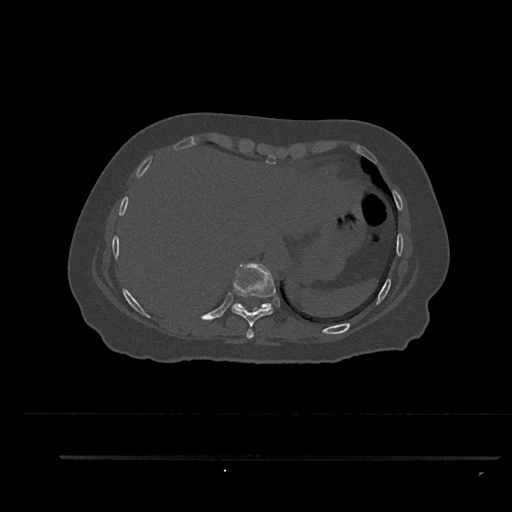
CT including the spine, one axial slice; slice 402 of 797 in the series (ordered by position); reconstruction kernel Br40s/3; 120 kVp; bone window (W 1800 / L 400 HU); 0.5 mm slice thickness; 512 × 512 image matrix, field of view 408 × 408 mm. Female patient, age 44 years. From the clinical record (not read from this slice): primary cancer: renal.
Outlined on this slice (semi-automatic segmentation, software-assisted and operator-edited):
- T10 vertebra: bounding box (x1, y1, x2, y2) in pixels: (234, 302, 272, 308)
- T8 vertebra: (246, 329, 254, 339)
- T9 vertebra: (231, 262, 275, 327)